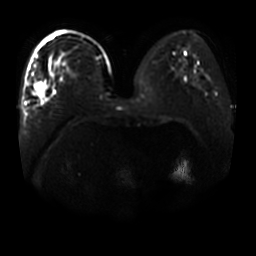
Breast MRI, one axial slice; position 20 of 44 along the scan axis; diffusion-weighted series; image 2 of 4 stored at this slice position (different b-values; order by instance number); 3 T; 5 mm slice thickness; 256 × 256 image matrix, field of view 400 × 400 mm. Female patient.
Structures marked on this image (manually delineated by an expert):
- tumour on diffusion-weighted imaging: box from (x=35, y=83) to (x=45, y=97) px